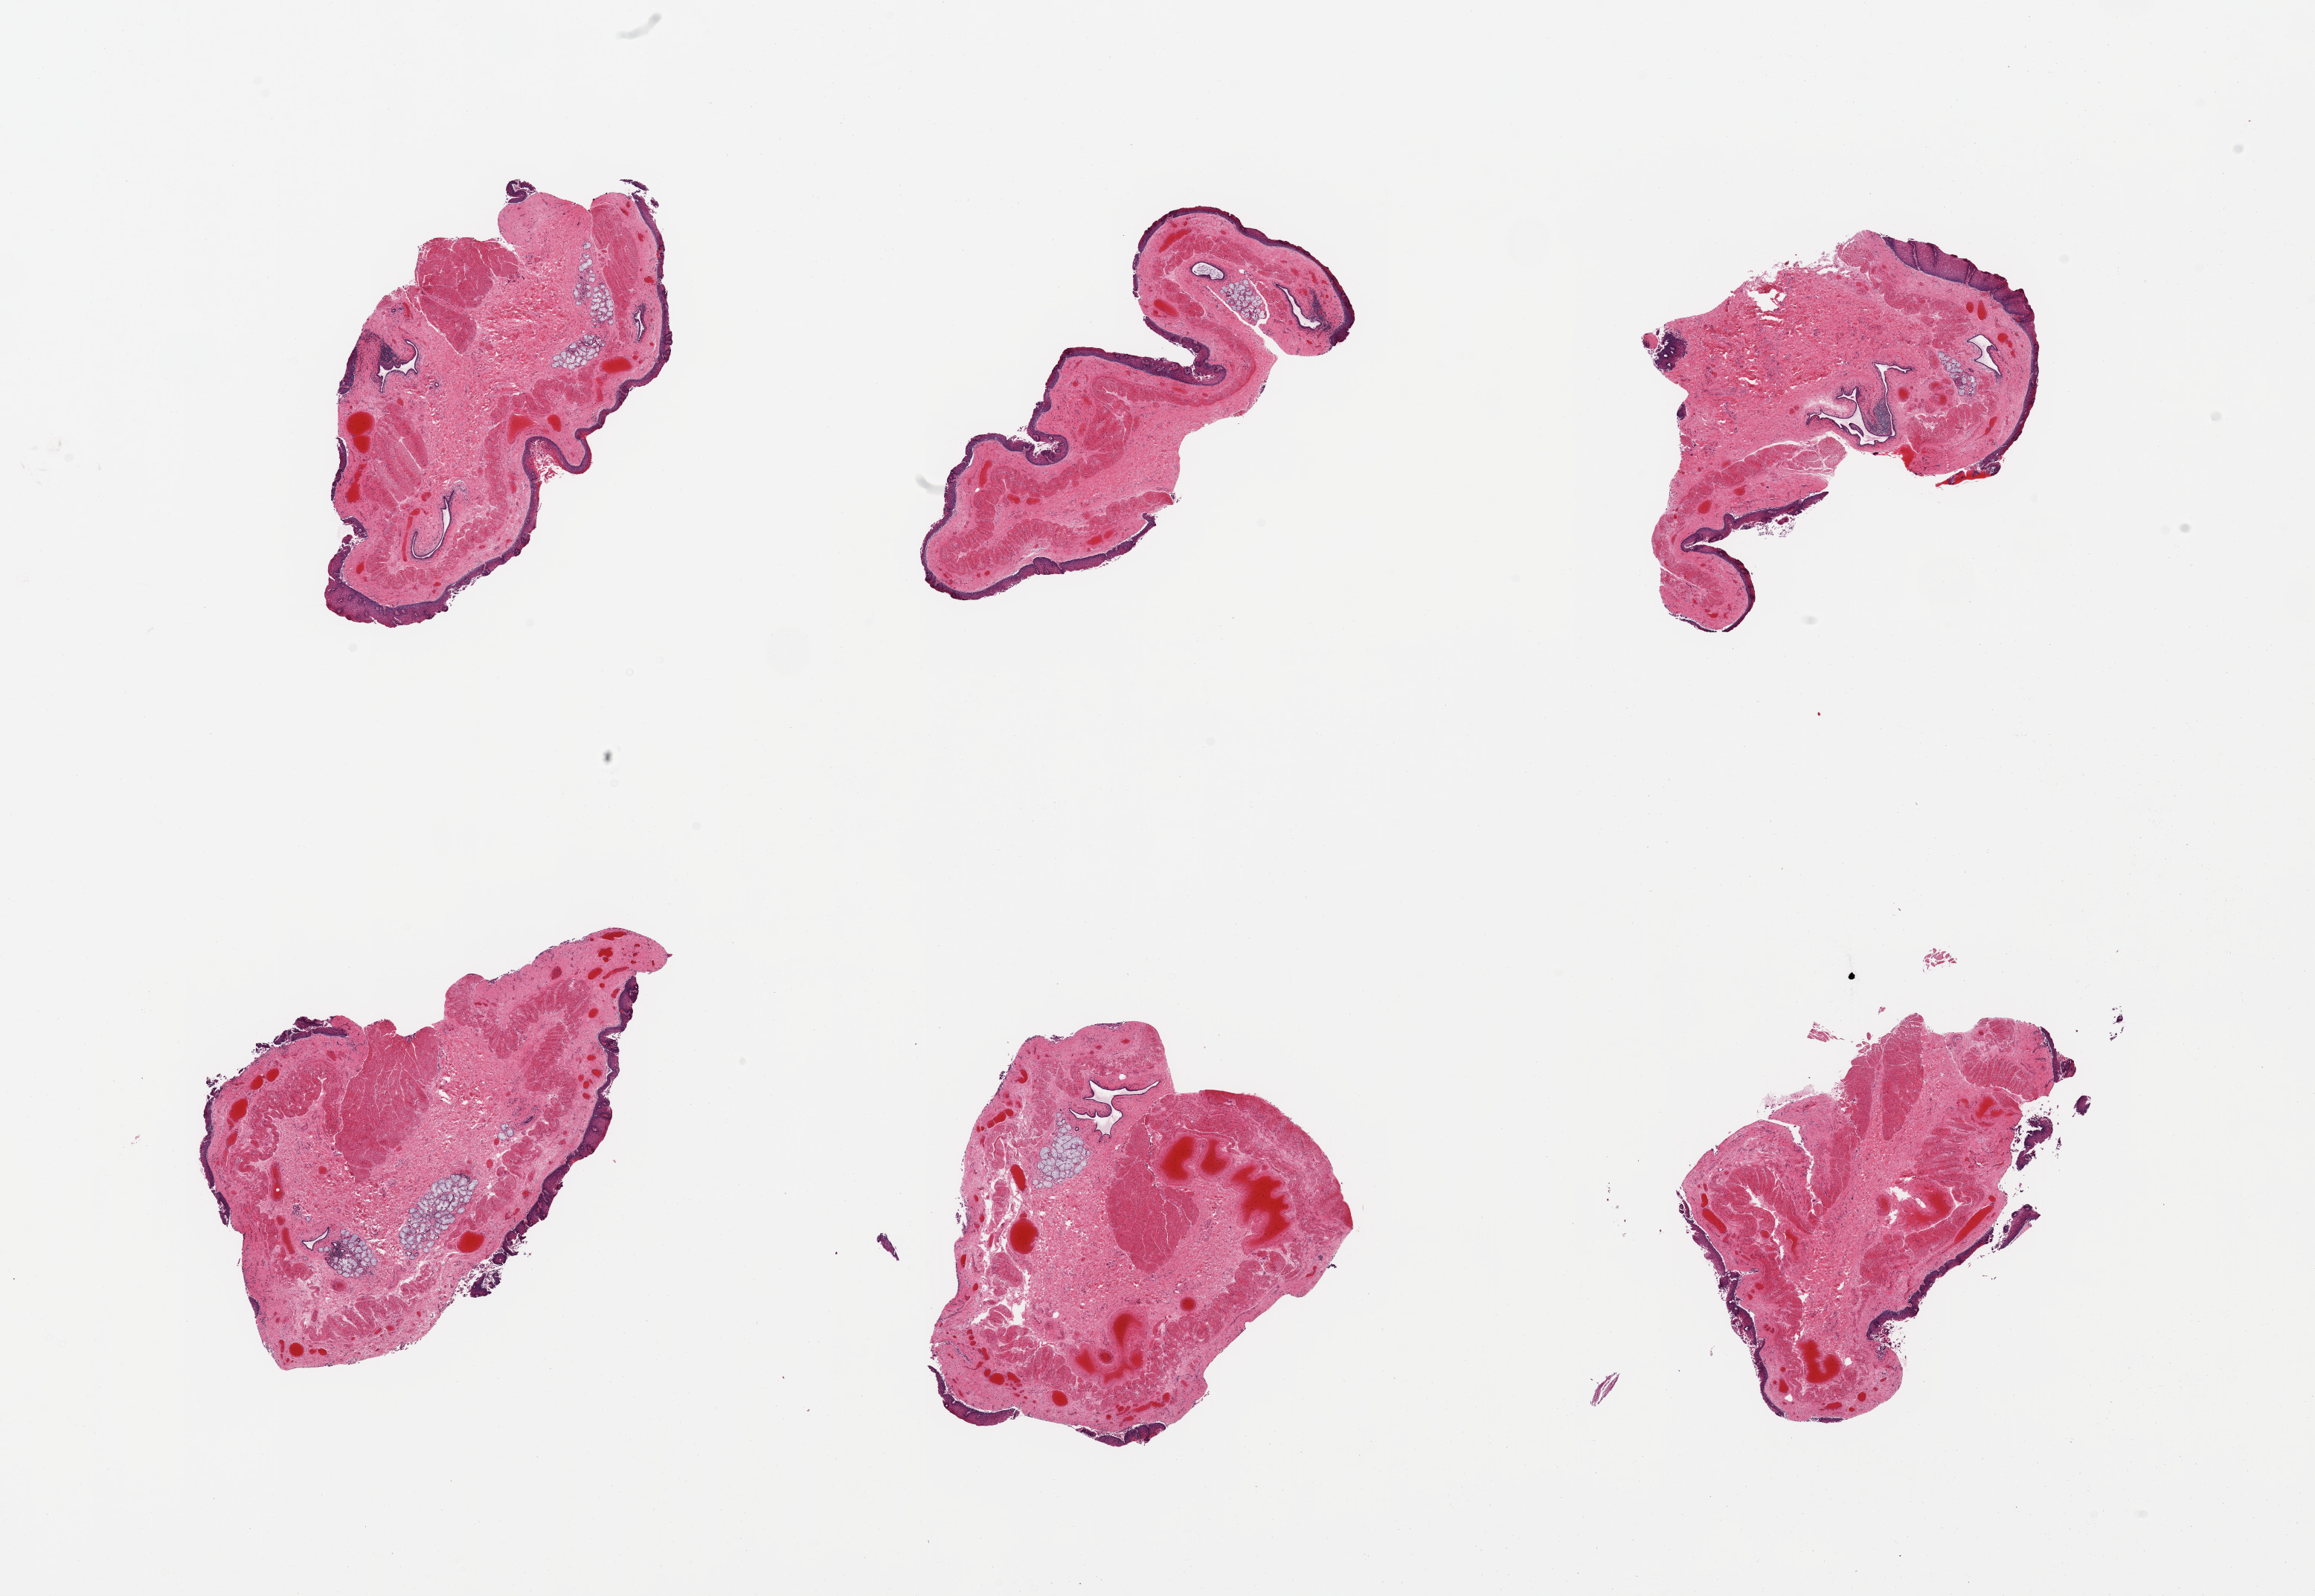
Whole-slide image, H&E stain, brightfield — a low-resolution overview of the entire scanned area, about 24.6 x 17.0 mm (acquisition: 20x scan), PAXgene-fixed paraffin-embedded (PFPE) section, target tissue: esophageal mucous membrane, tissue donor sample. Donor: male.
Reviewer comment on this tissue sample: 6 pieces, squamous mucosa partially sloughing, poorly preserved, few submucosal mucus glands.